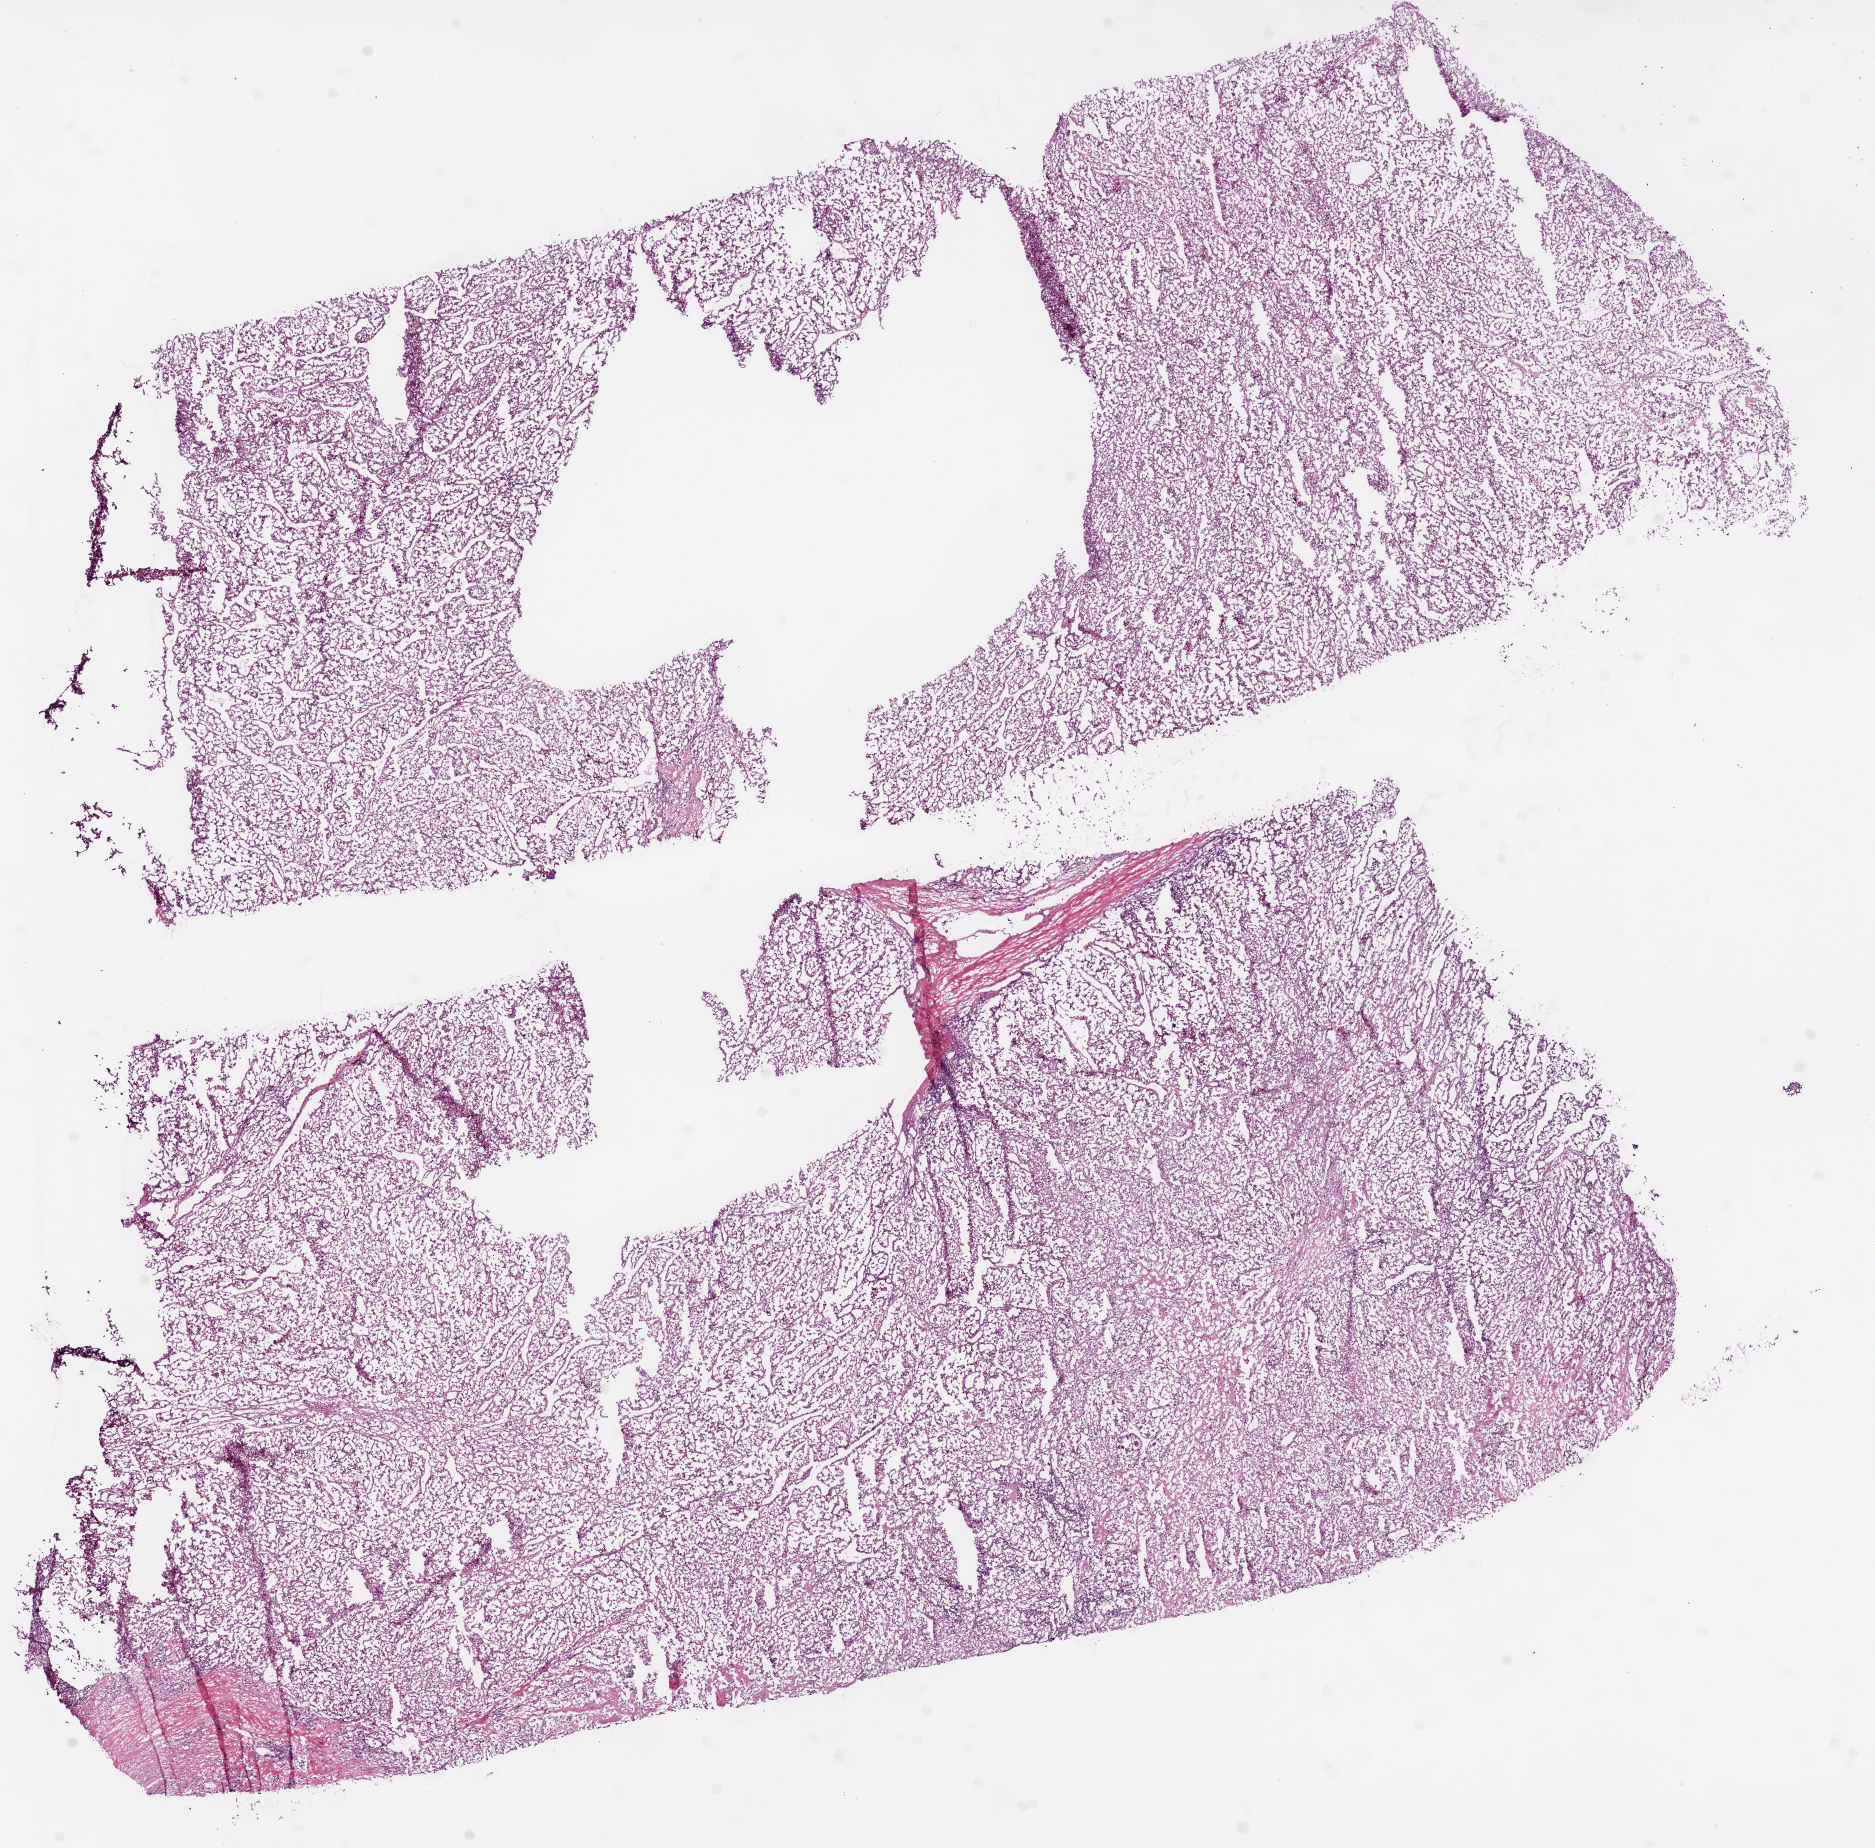
Digitized H&E-stained tissue section (whole slide) — a low-resolution overview of the entire scanned area, about 15.0 x 14.8 mm; frozen section from the bottom of the tissue portion; kidney, primary tumour sample. Patient: male, age at initial diagnosis 57 years. Histologic grade: G4 (undifferentiated). Composition of this section per pathologist review: tumour cells 97%, tumour nuclei 80%, stromal cells 3%, necrosis 0%.
Laterality: right. Histologic diagnosis: Clear cell adenocarcinoma, NOS. Lymph nodes positive (case pathology): 2 of 16 examined. AJCC pathologic stage: III.